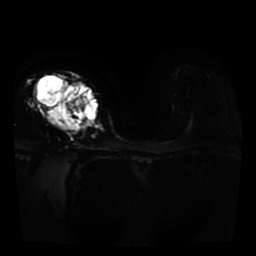
Breast MRI, one axial slice. Position 25 of 41 along the scan axis. Diffusion-weighted series; image 2 of 4 stored at this slice position (different b-values; order by instance number). 1.5 T. 5 mm slice thickness. 256 × 256 image matrix, field of view 330 × 330 mm. Female patient.
Structures marked on this image (manually delineated by an expert):
- tumour on diffusion-weighted imaging: bounding box [x1, y1, x2, y2] px = [44, 78, 73, 130]